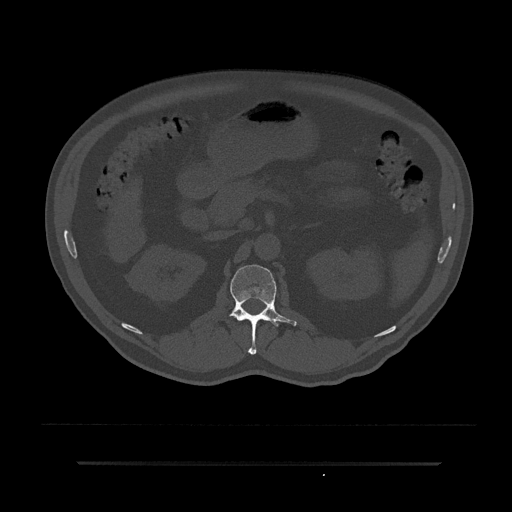
CT including the spine, one axial slice. Slice 145 of 797 in the series (ordered by position). 120 kVp. Bone window (W 1800 / L 400 HU). 0.5 mm slice thickness. 512 × 512 image matrix. Patient: male, 59 years. Case-level facts recorded for this patient, not image findings: primary cancer: bile ducts; vertebrae with lytic lesions (as recorded): T10.
Annotated regions visible in this slice (semi-automatic segmentation, software-assisted and operator-edited):
- L1 vertebra: bounding box (x1, y1, x2, y2) in pixels: (228, 265, 297, 355)